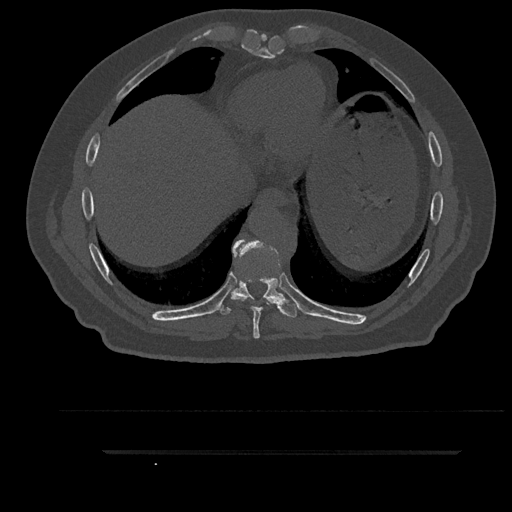
CT including the spine, one axial slice. Position 446 of 797 along the scan axis. Reconstruction kernel Br40s/3. 120 kVp. Bone window (W 1800 / L 400 HU). 512 × 512 image matrix. Male patient, age 63 years. From the clinical record (not read from this slice): primary cancer: renal.
Outlined on this slice (semi-automatic segmentation, software-assisted and operator-edited):
- T10 vertebra: box from (x=281, y=293) to (x=284, y=296) px
- T8 vertebra: (x=231, y=239)–(x=279, y=339)
- T9 vertebra: (x=214, y=249)–(x=298, y=318)